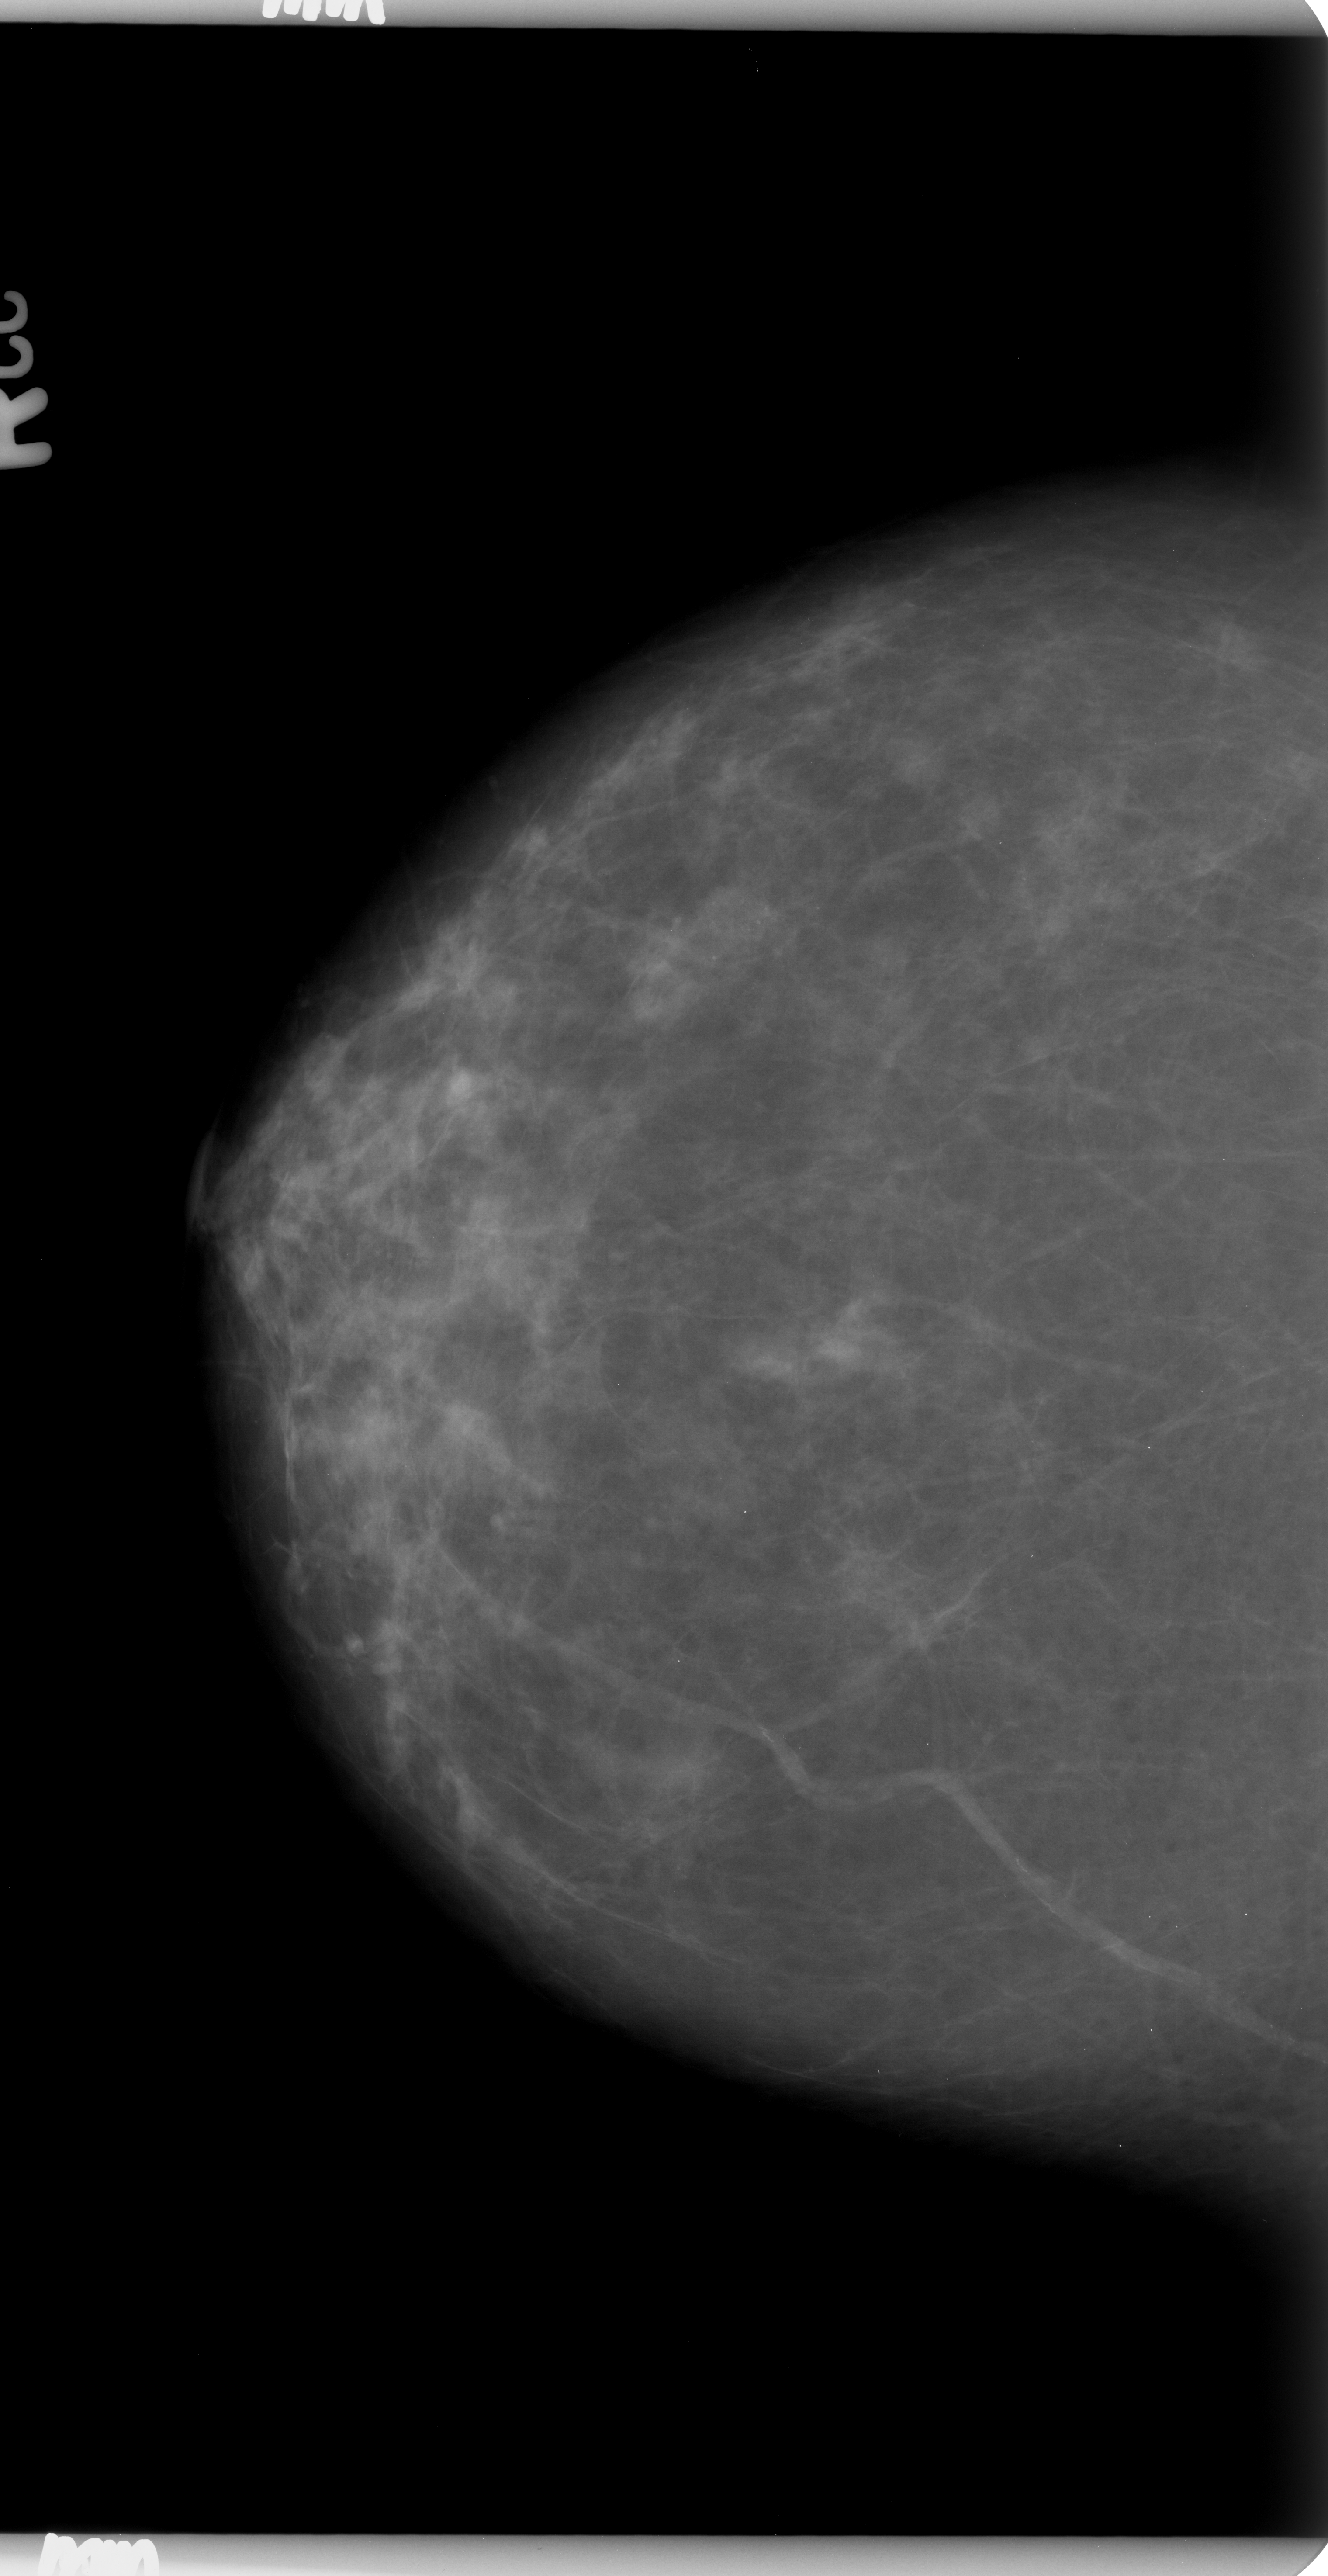
Scanned film-screen mammogram, right breast, CC view, BI-RADS breast density category 2 (scale 1–4).
- Radiologist-marked abnormalities on this image: calcifications, morphology round and regular, distribution clustered; BI-RADS assessment category 3; pathology result (as recorded, not read from the image): benign.